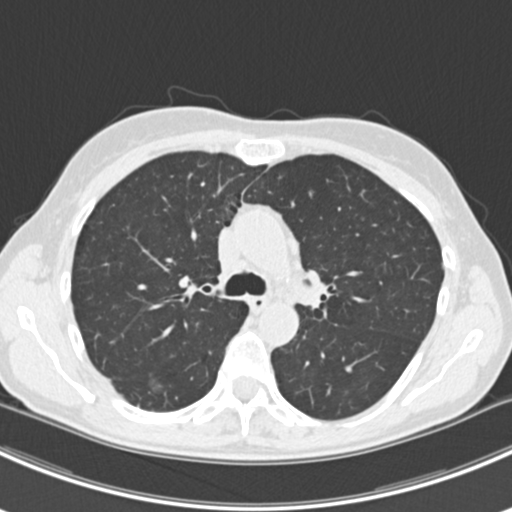
Axial slice from a low-dose chest CT screening exam, baseline screening round, lung window (W 1500 / L -600 HU), standard (soft-tissue) reconstruction kernel (B30f). Female participant, aged 63 years at enrolment. Current smoker at enrolment.
Lesion marked by an expert reader, box from (x=135, y=366) to (x=177, y=402) px. The screening reader recorded 10 non-calcified nodules or masses ≥4 mm on this exam; which of them this box marks is not recorded. Participant outcome: lung cancer diagnosed 751 days after this screen — bronchiolo-alveolar adenocarcinoma, NOS, right upper lobe, right middle lobe, right lower lobe, left upper lobe, left lower lobe, moderately differentiated (G2), stage IV (AJCC 6th edition).